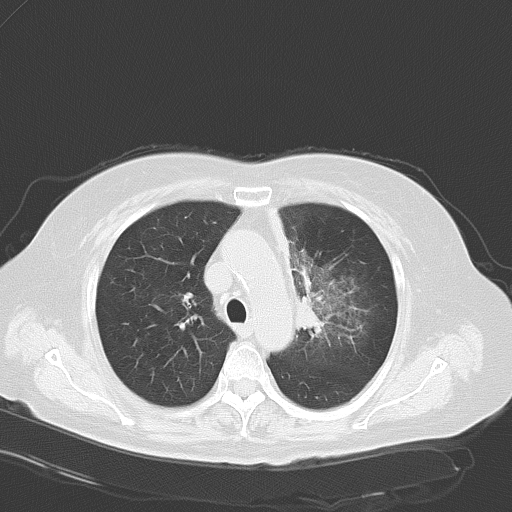
Chest CT, one axial slice; slice 40 of 56 in the series (ordered by position); reconstruction kernel B70f; 120 kVp; lung window (W 1500 / L -600 HU); 5 mm slice thickness; 512 × 512 image matrix, field of view 353 × 353 mm. Patient: female, 65 years. Case-level facts recorded for this patient, not image findings: clinical TNM (as recorded): T2b N1 M0.
Outlined on this slice (bounding box drawn by a radiologist):
- lung tumour (recorded histology: adenocarcinoma): bounding box <297,286,326,339> (left, top, right, bottom; pixels)